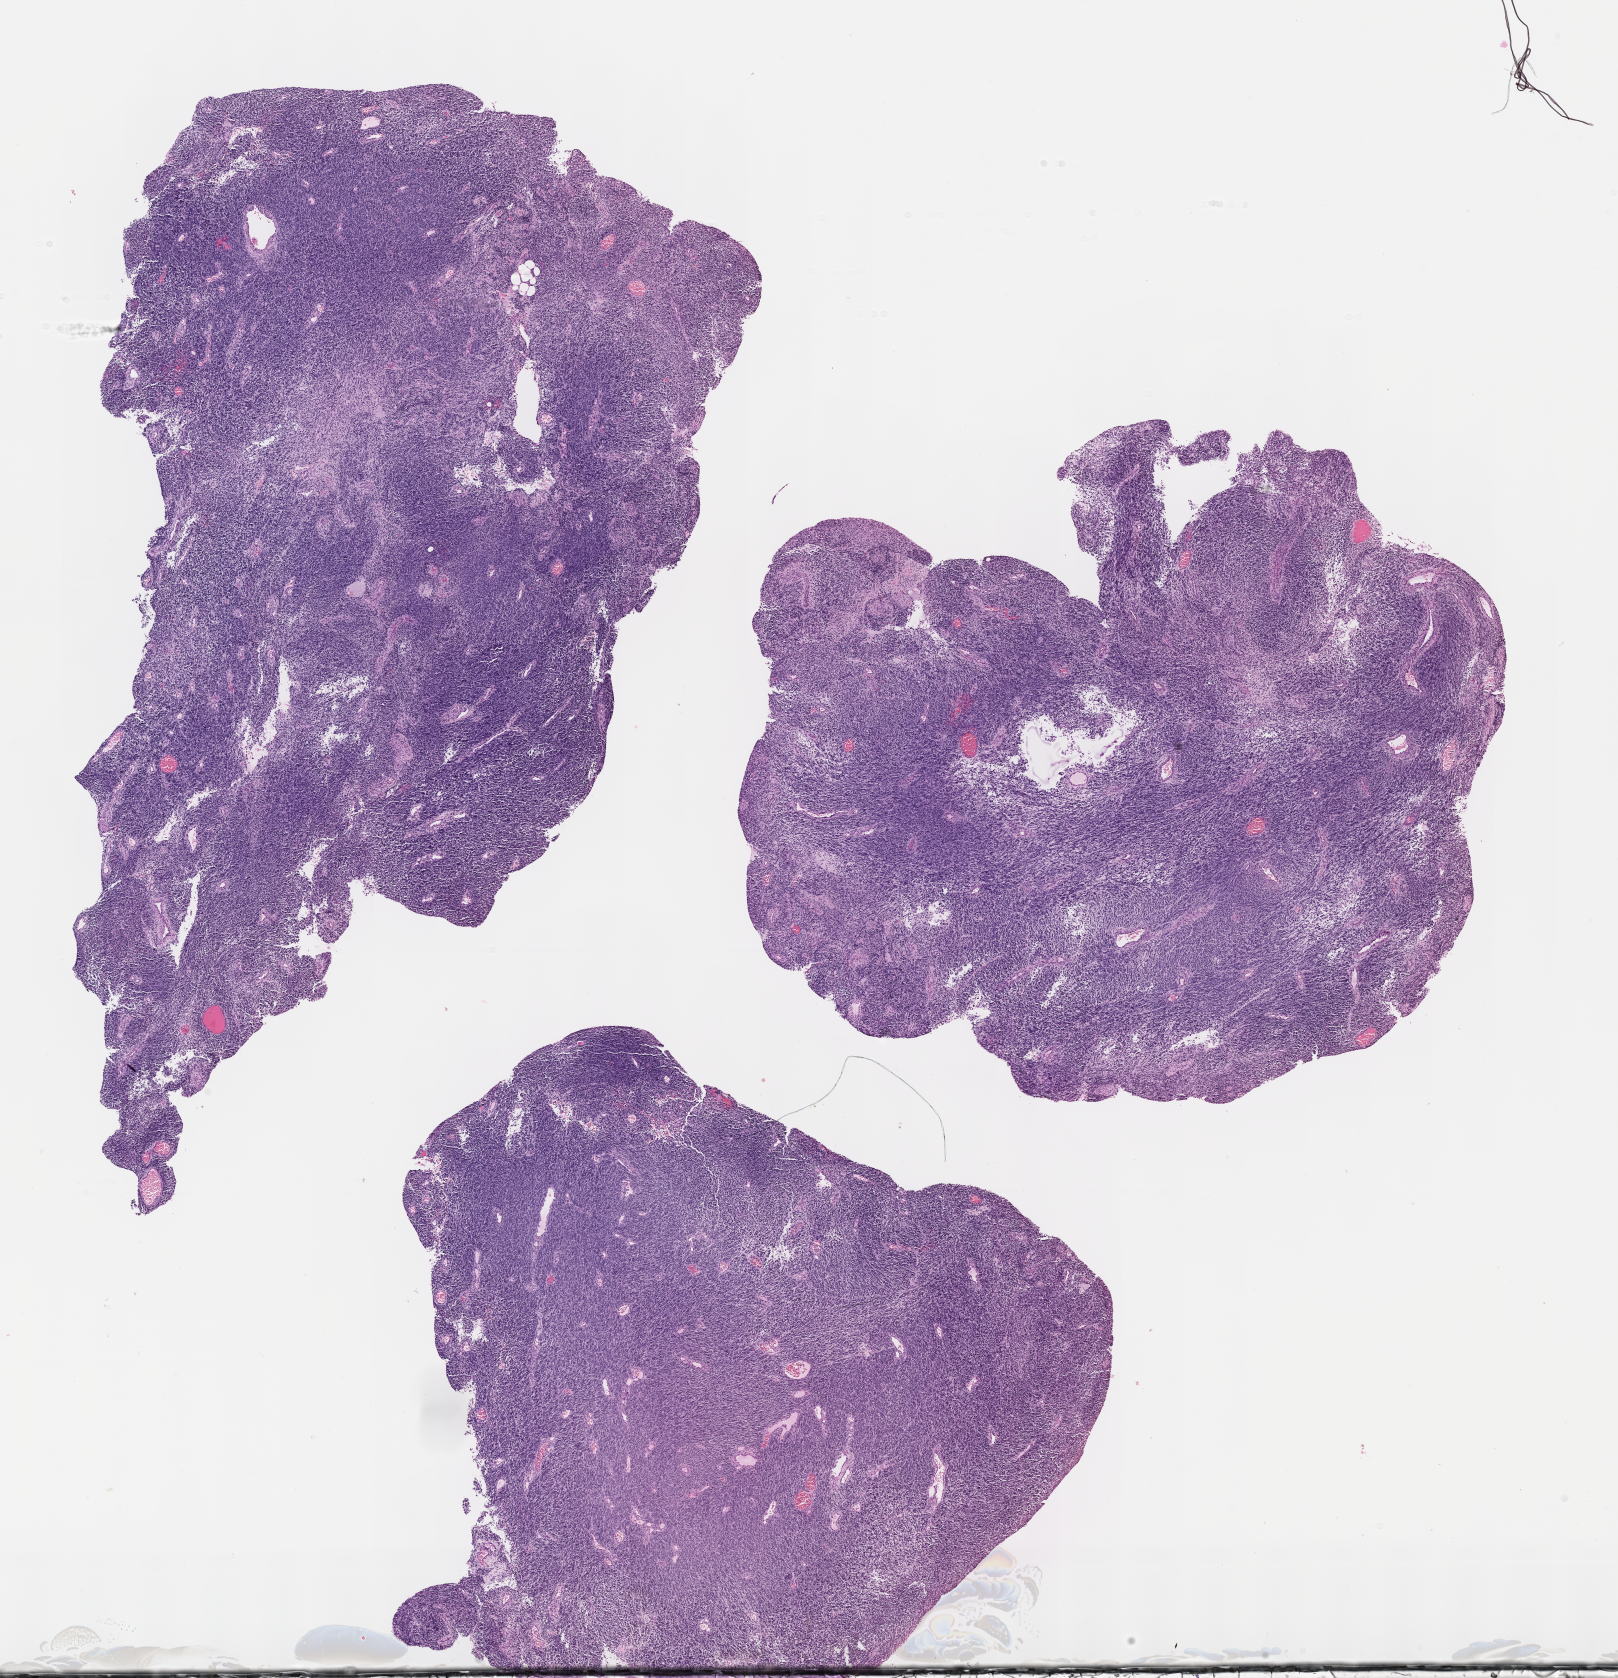
Digitized haematoxylin and eosin-stained section of tumor tissue — whole scanned area (about 13.1 x 13.6 mm) shown as a low-resolution overview, formalin-fixed, paraffin-embedded (FFPE) tissue, site: soft tissue, shoulder-left. Patient: male, age 0.3 years at diagnosis.
Diagnosis: rhabdomyosarcoma; histological classification: embryonal rhabdomyosarcoma. Primary site (case record): shoulder girdle. Stage (as recorded): 3. Metastatic status at presentation (as recorded): non-metastatic (confirmed).